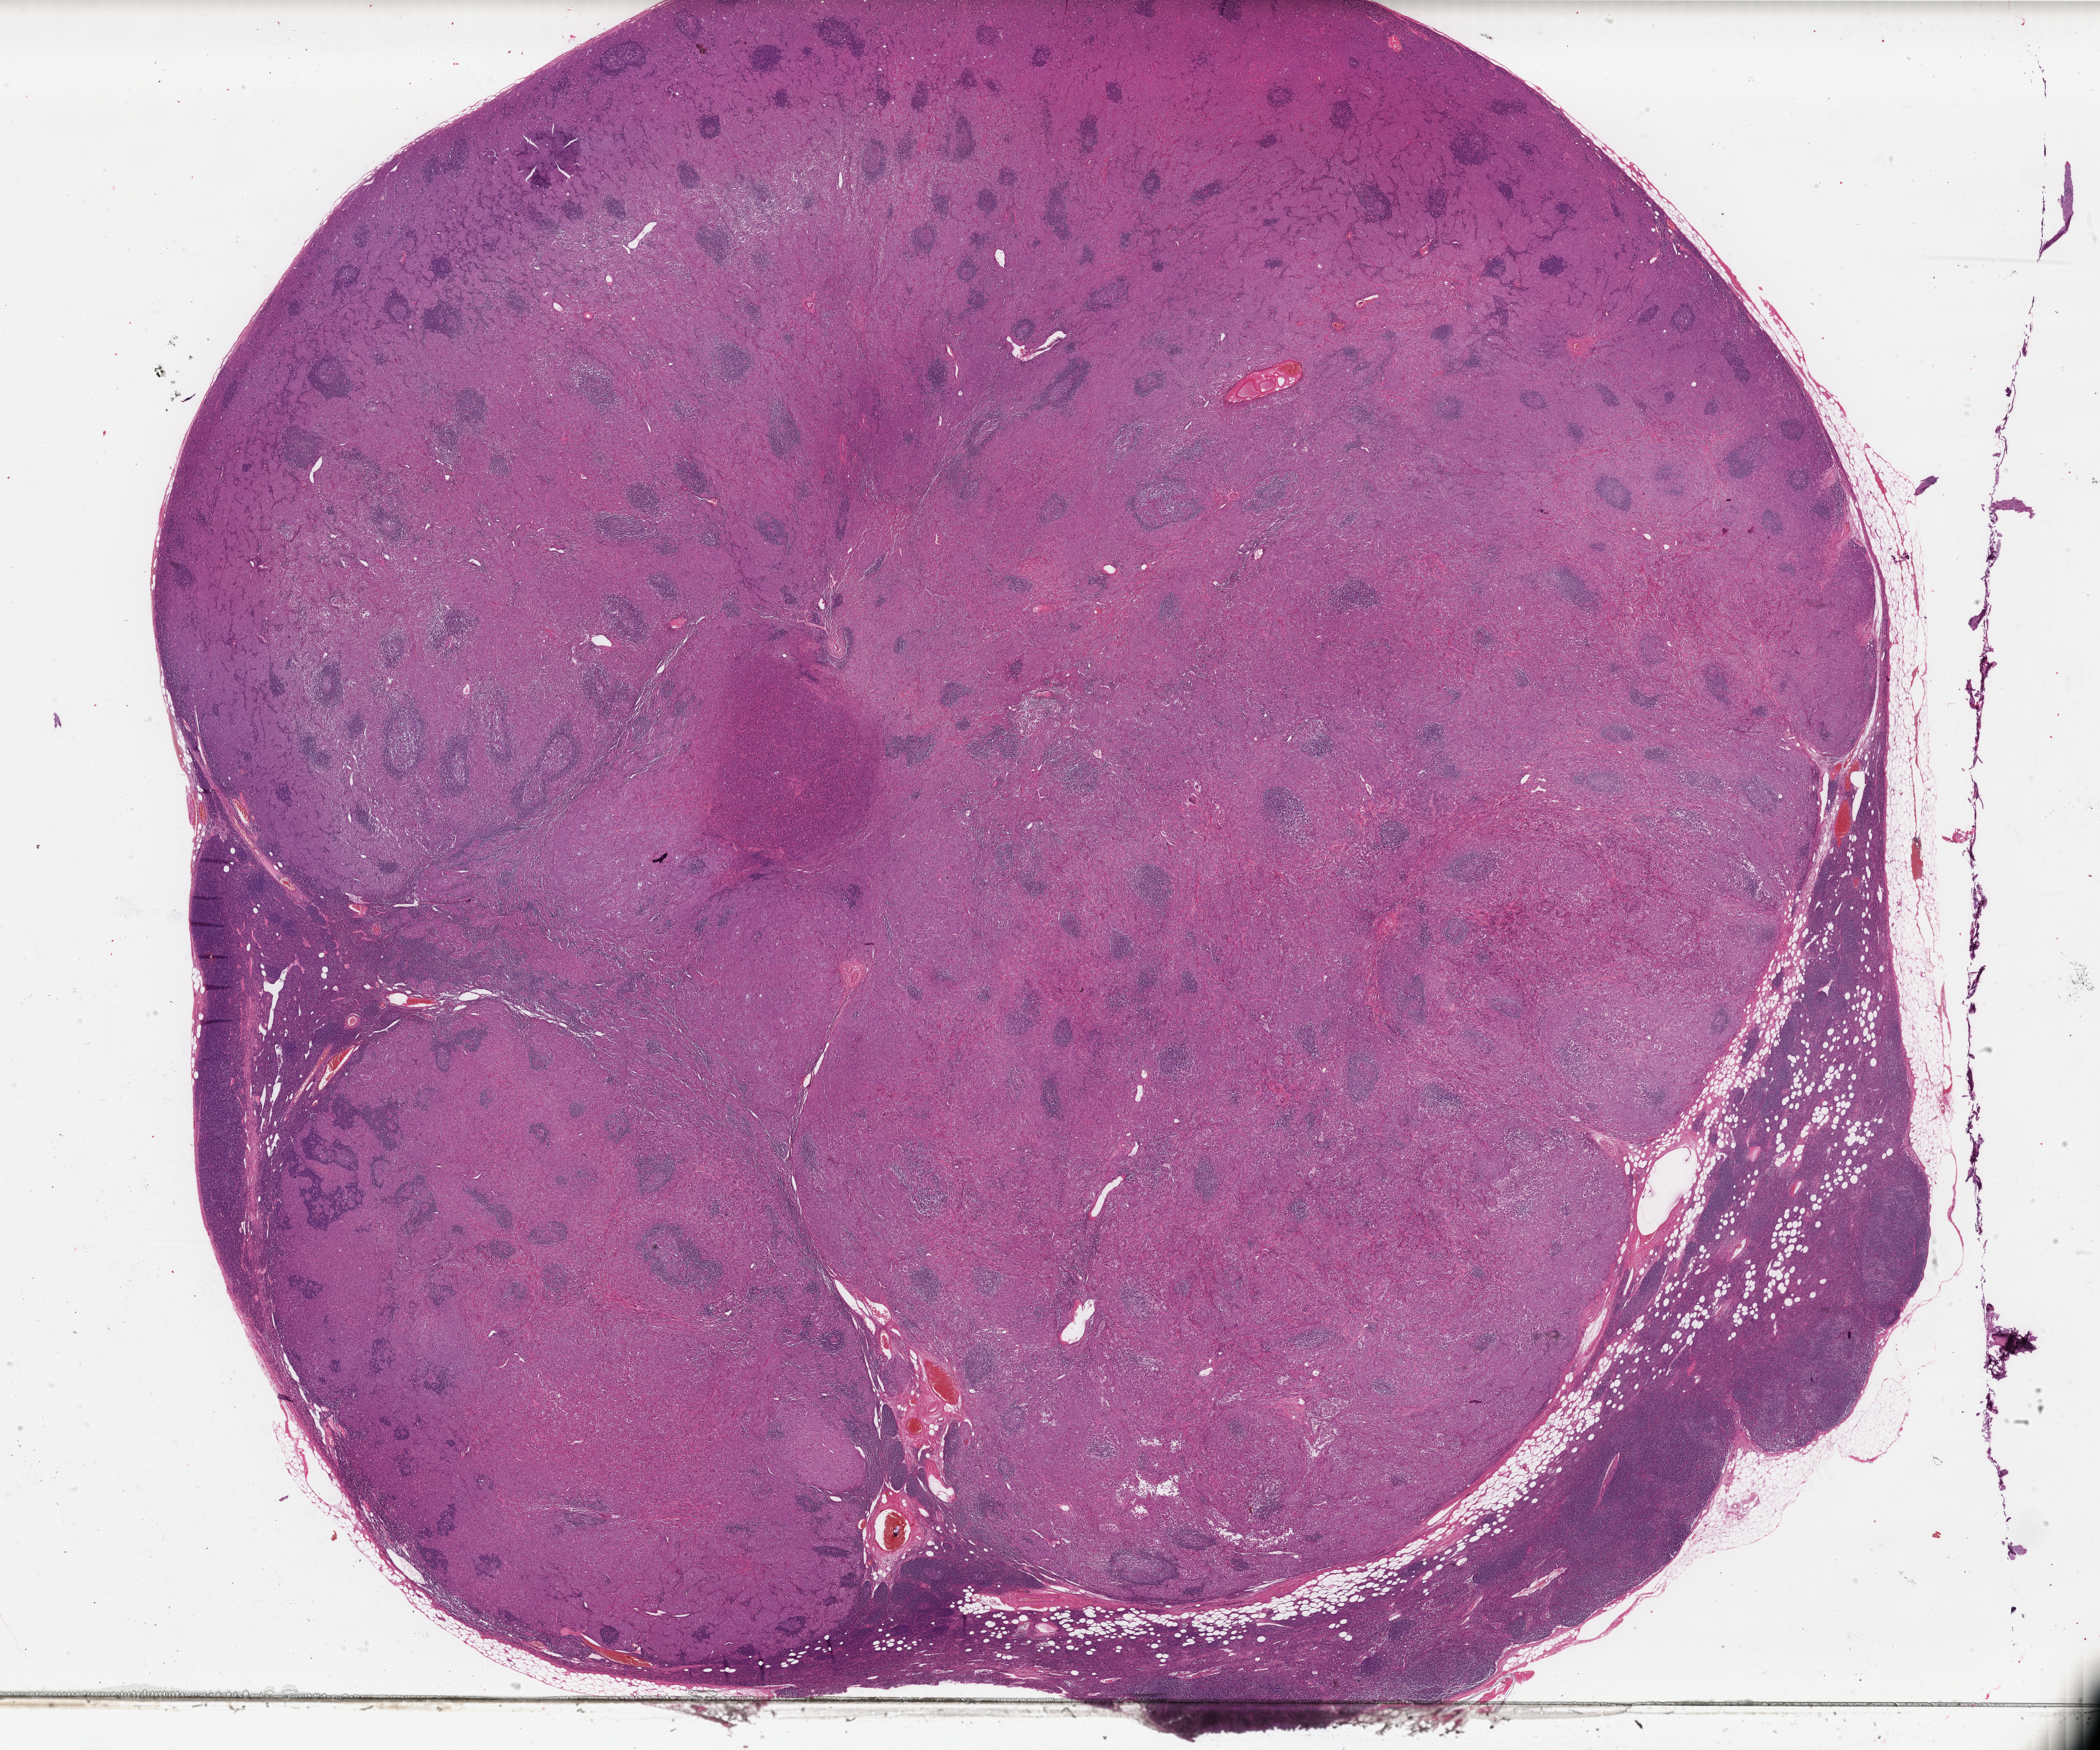
Digitized Hematoxylin and eosin (H&E) stained tissue section (whole slide) — whole scanned area (about 28.6 x 23.8 mm) shown as a low-resolution overview; formalin-fixed paraffin-embedded (FFPE) diagnostic section; sample: primary tumour, skin. Patient: female, age at initial diagnosis 40 years.
• pathologic diagnosis: Malignant melanoma, NOS